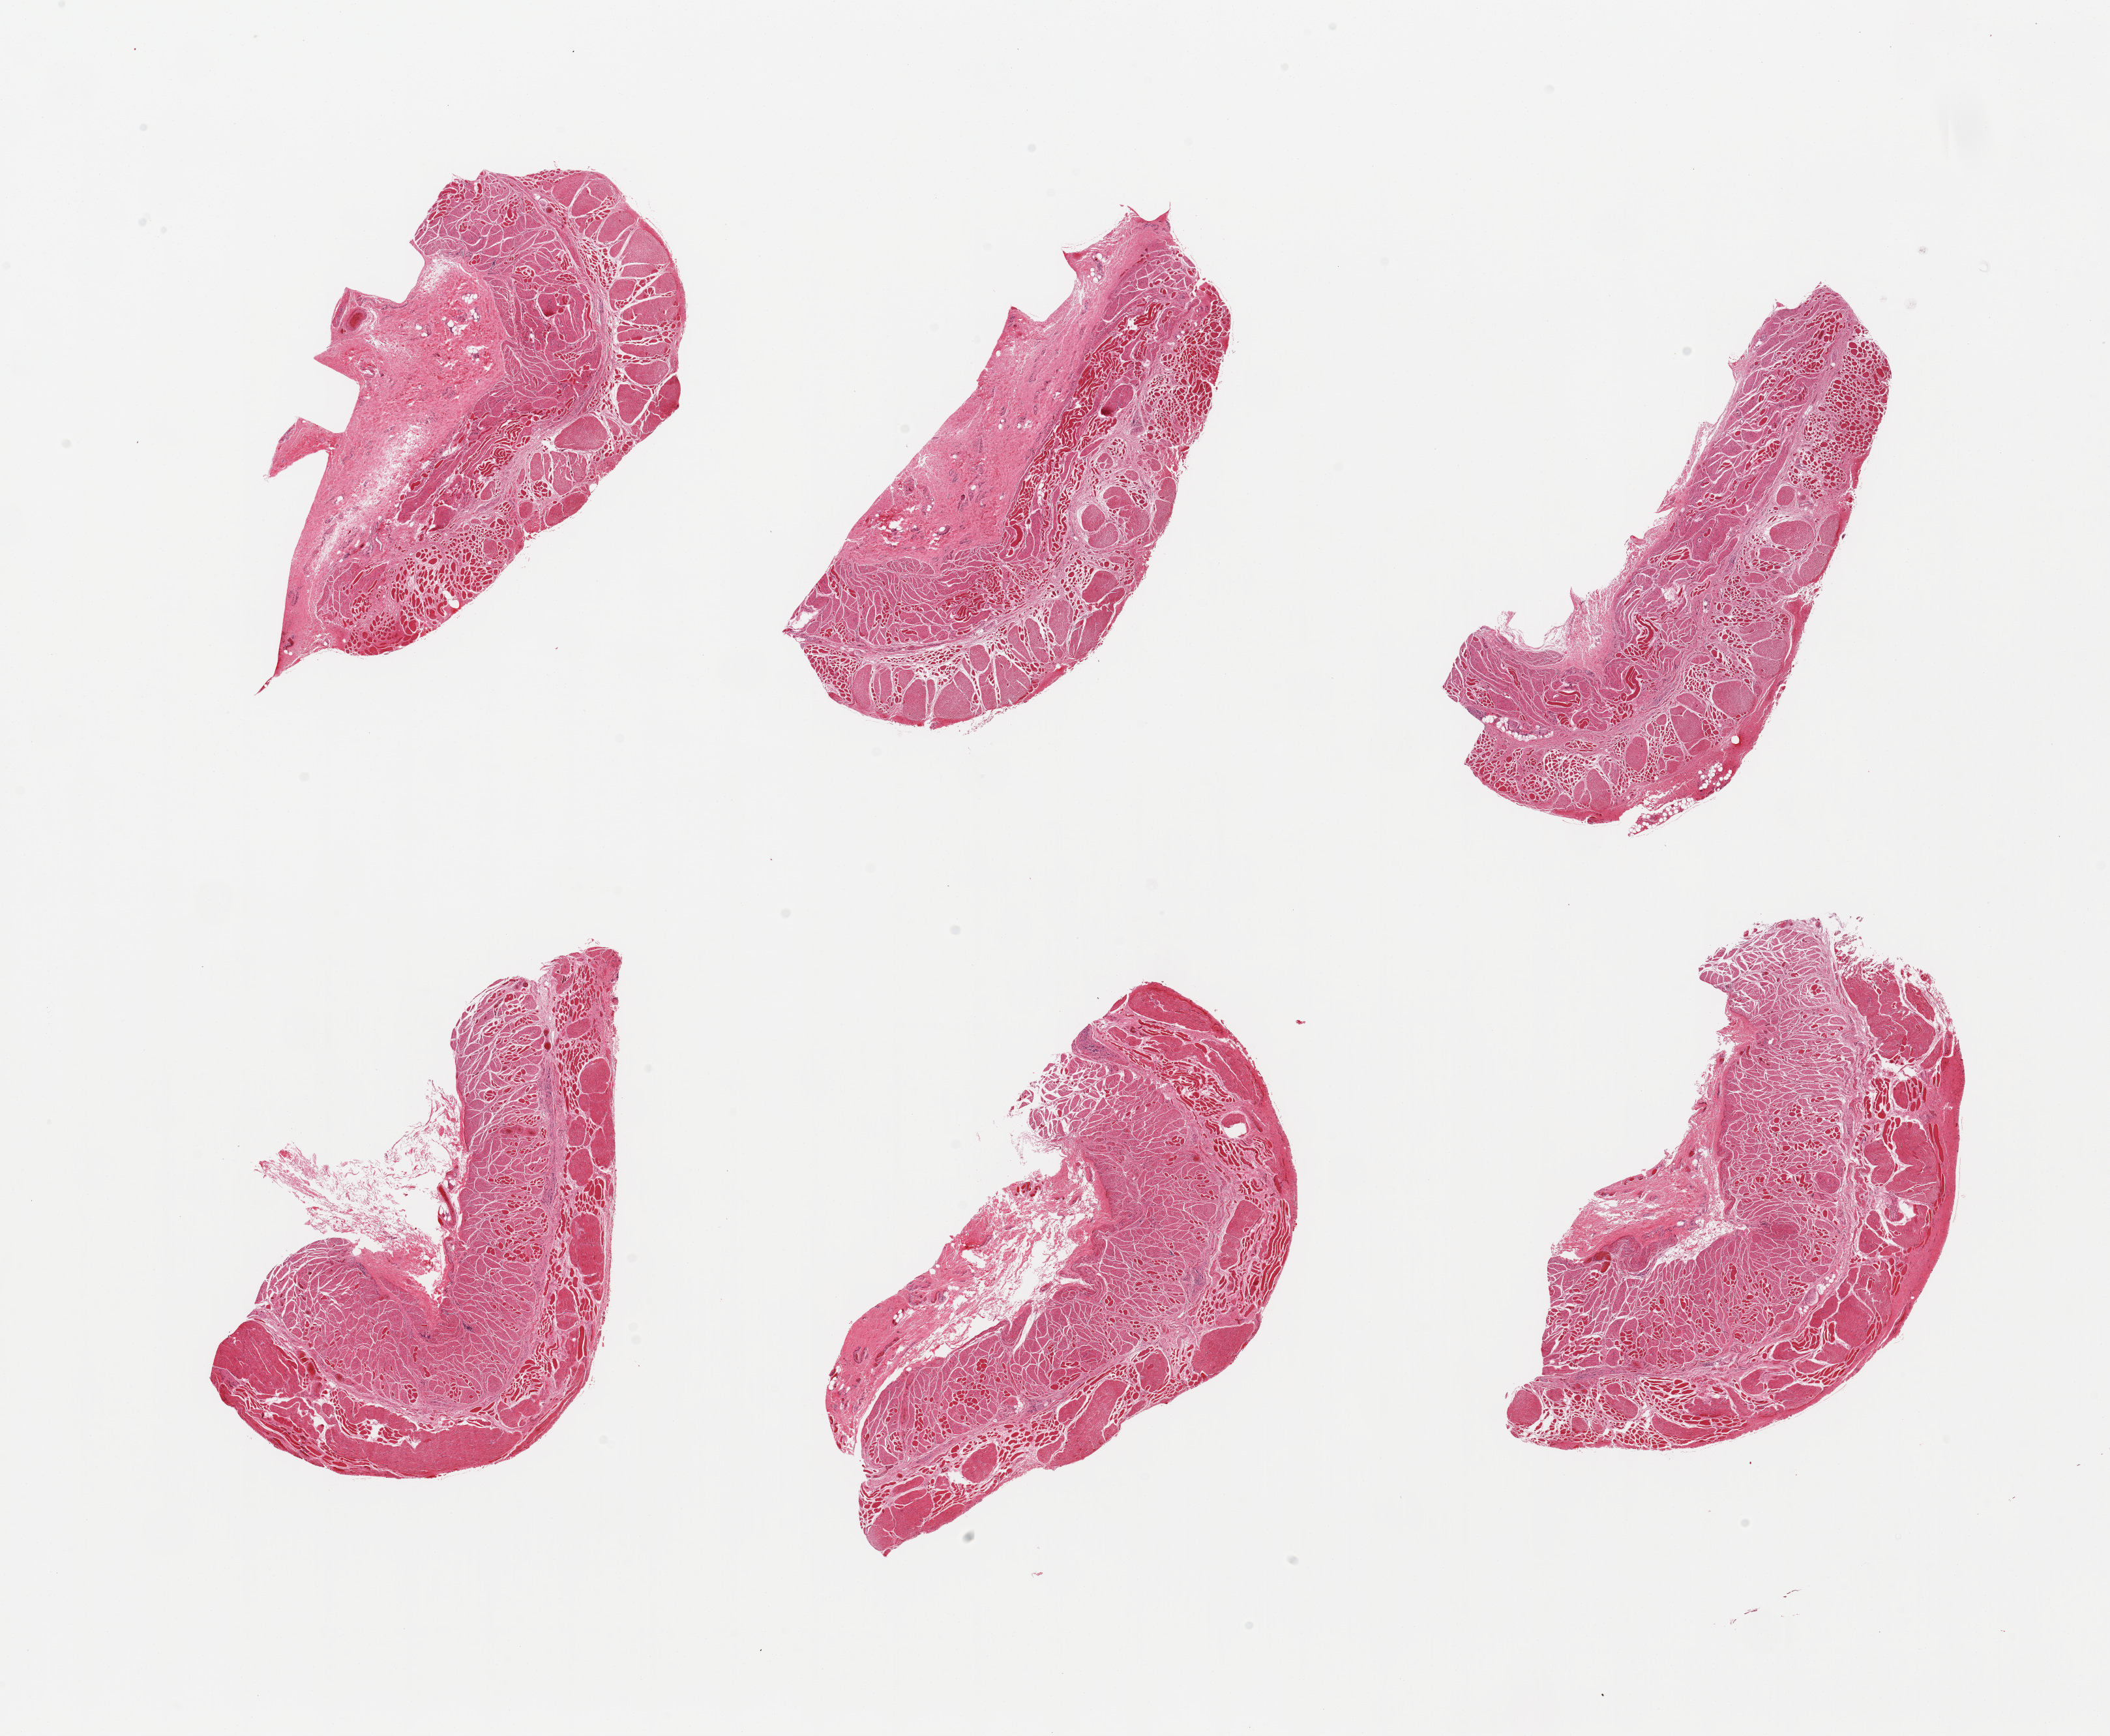
Hematoxylin and eosin (H&E) whole-slide image, brightfield, shown as a low-resolution overview of the whole scanned area (about 25.6 x 21.1 mm, acquisition: 20x scan). PAXgene-fixed paraffin-embedded (PFPE) section. Target tissue: esophageal muscle. Tissue donor sample. Donor: male.
• reviewer comment on this tissue sample: 6 pieces; 30% admixed skeletal muscle